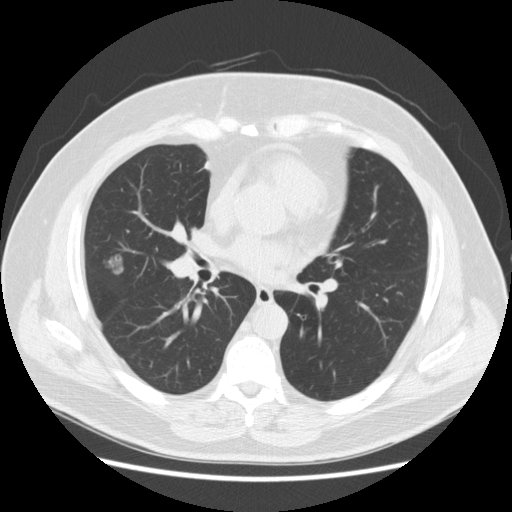
Axial slice from a low-dose chest CT screening exam. Baseline annual screen. Lung window (W 1500 / L -600 HU). 2.5 mm slice thickness. Standard (soft-tissue) reconstruction kernel (STANDARD). 512 × 512 image matrix. Male, age 67 years at enrolment. Former smoker at enrolment.
• Expert reader's lesion annotation, bounding box <92,250,131,287> (left, top, right, bottom; pixels).
• Screening reader's record for this exam (one nodule recorded; not confirmed to be the boxed lesion): non-calcified nodule or mass ≥4 mm, right middle lobe, 15 × 11 mm, smooth margins, soft tissue attenuation.
• Official screen result: positive, change unspecified: nodule(s) >= 4 mm or enlarging nodule(s), mass(es), or other non-specific abnormalities suspicious for lung cancer.
• Lung cancer was diagnosed 409 days after this screen: adenocarcinoma, NOS, right middle lobe, moderately differentiated (G2), stage IA (AJCC 6th edition), 14 mm at pathology.